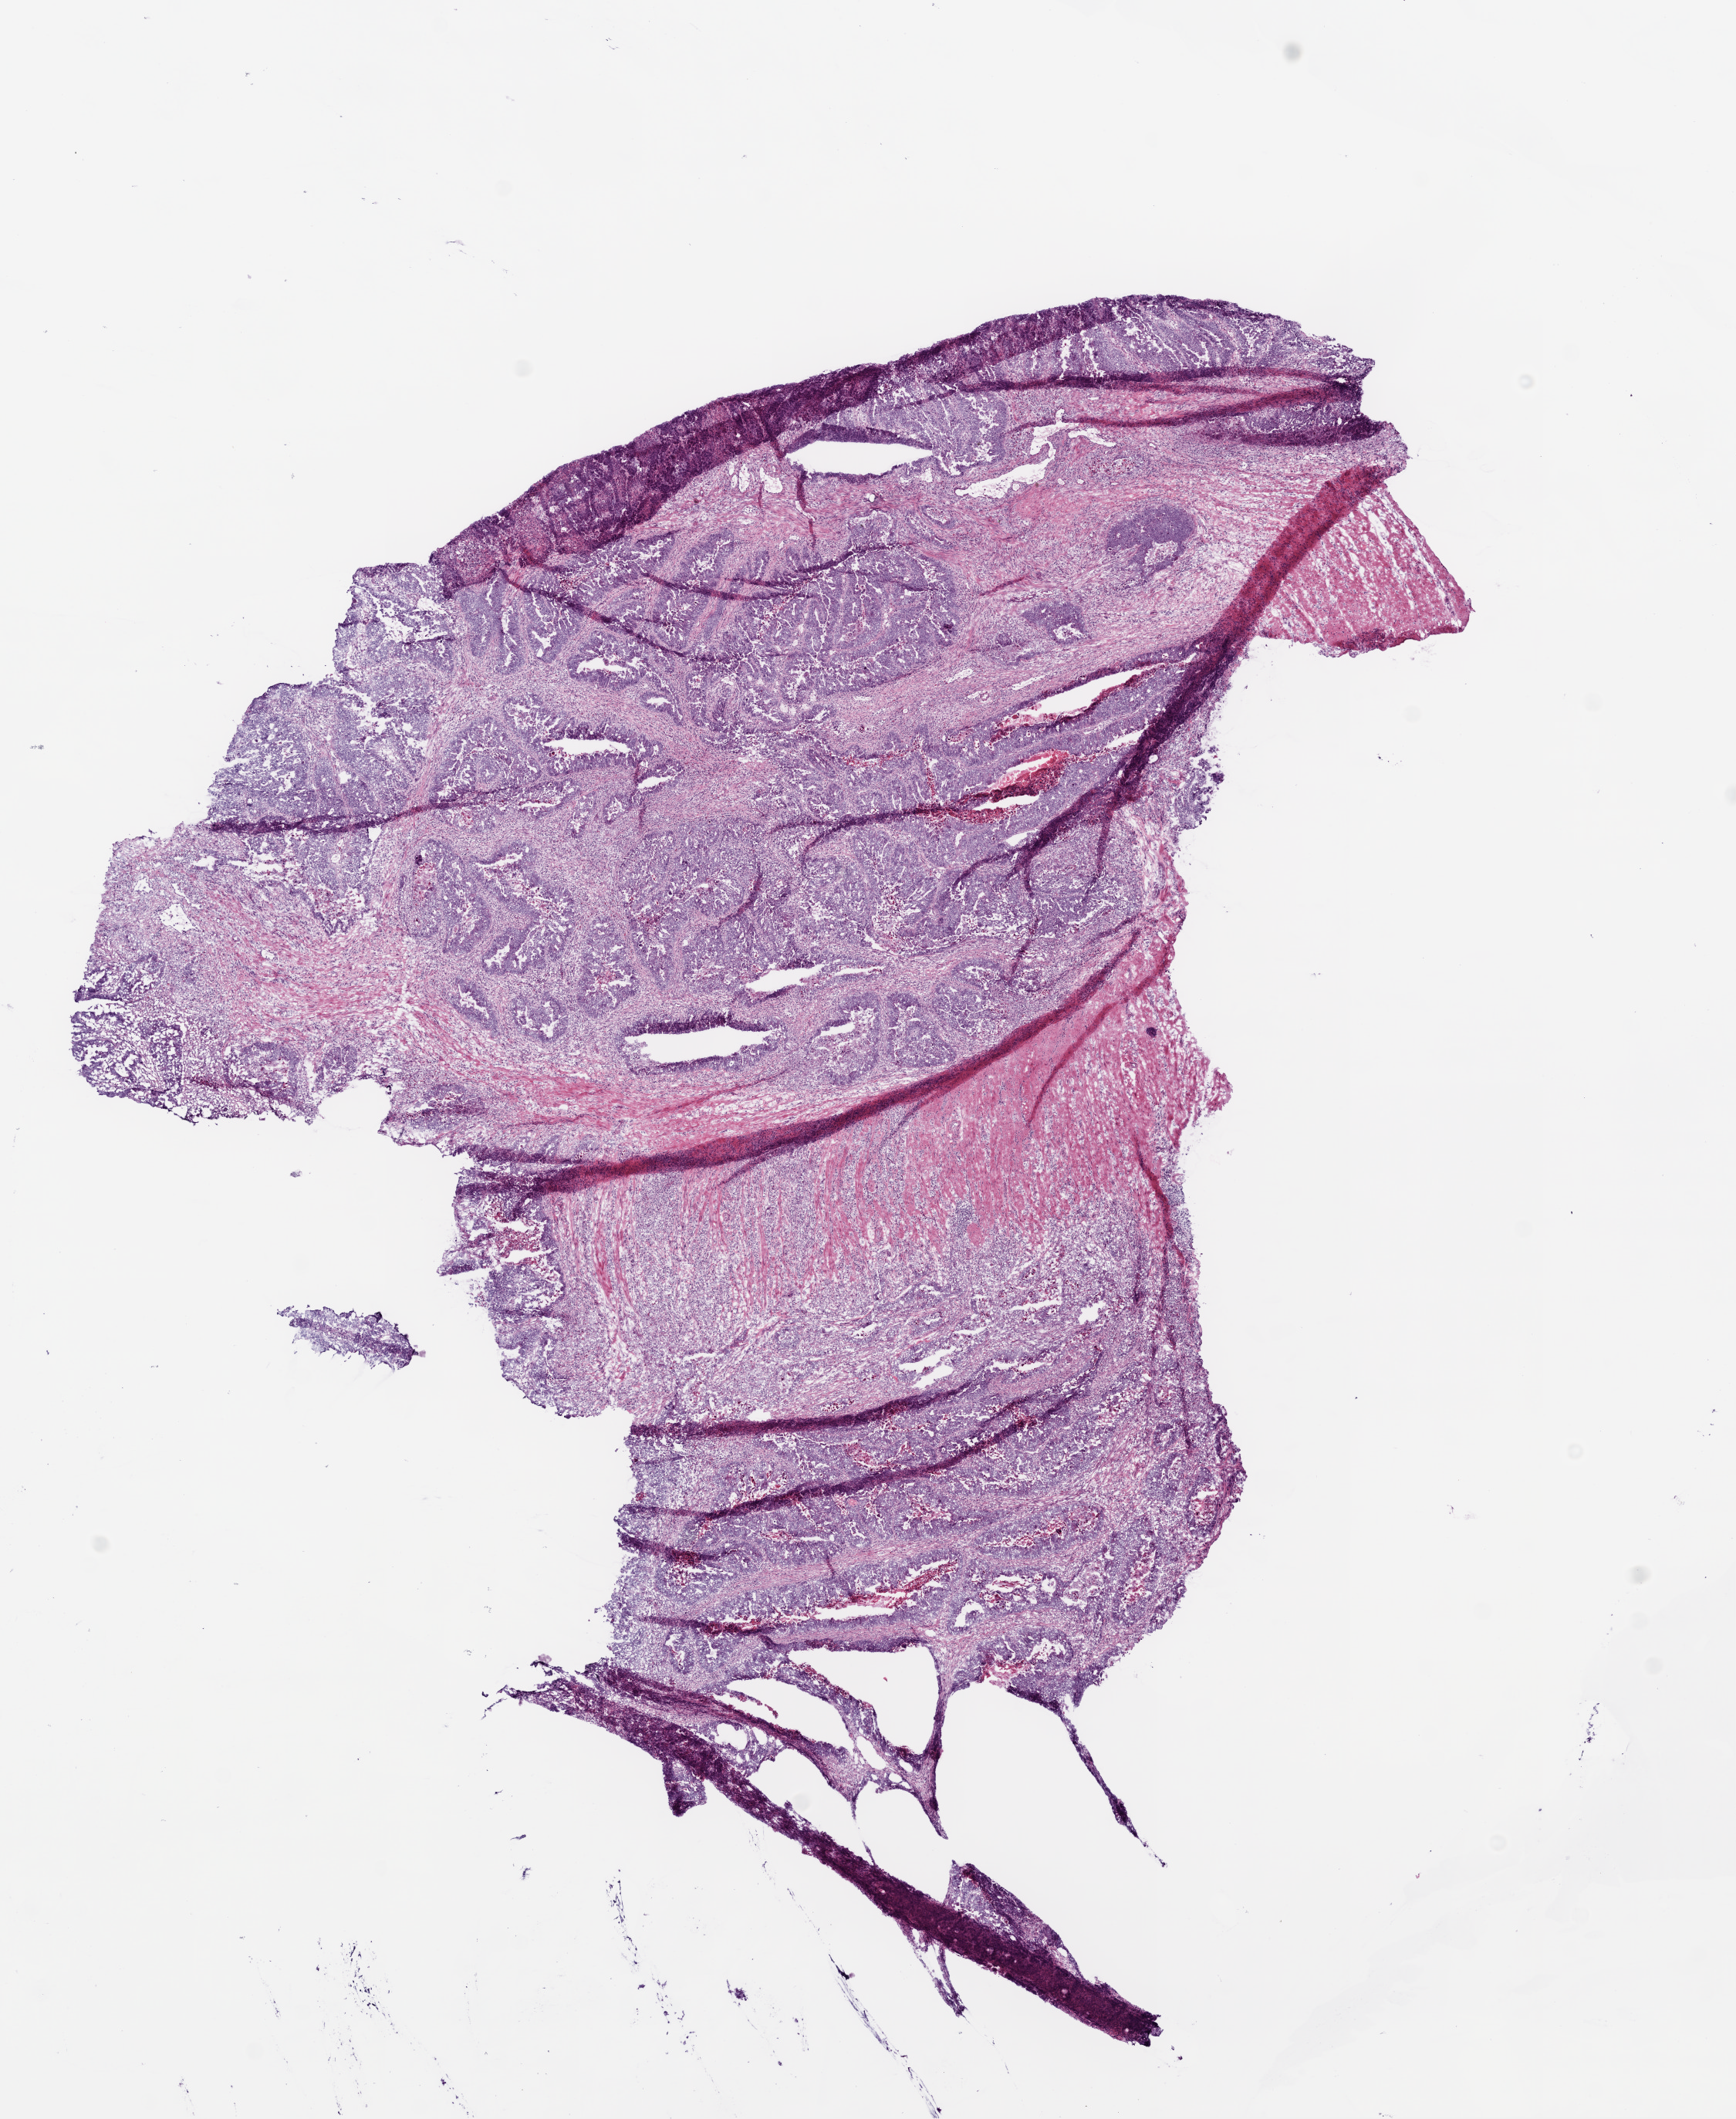
Digitized H&E tissue section (whole slide), low-resolution overview of the scanned area, about 9.0 x 11.0 mm. Frozen section from the bottom of the tissue portion. Rectum, primary tumour sample. Patient: male, age at initial diagnosis 61 years.
Diagnosis: Adenocarcinoma, NOS.